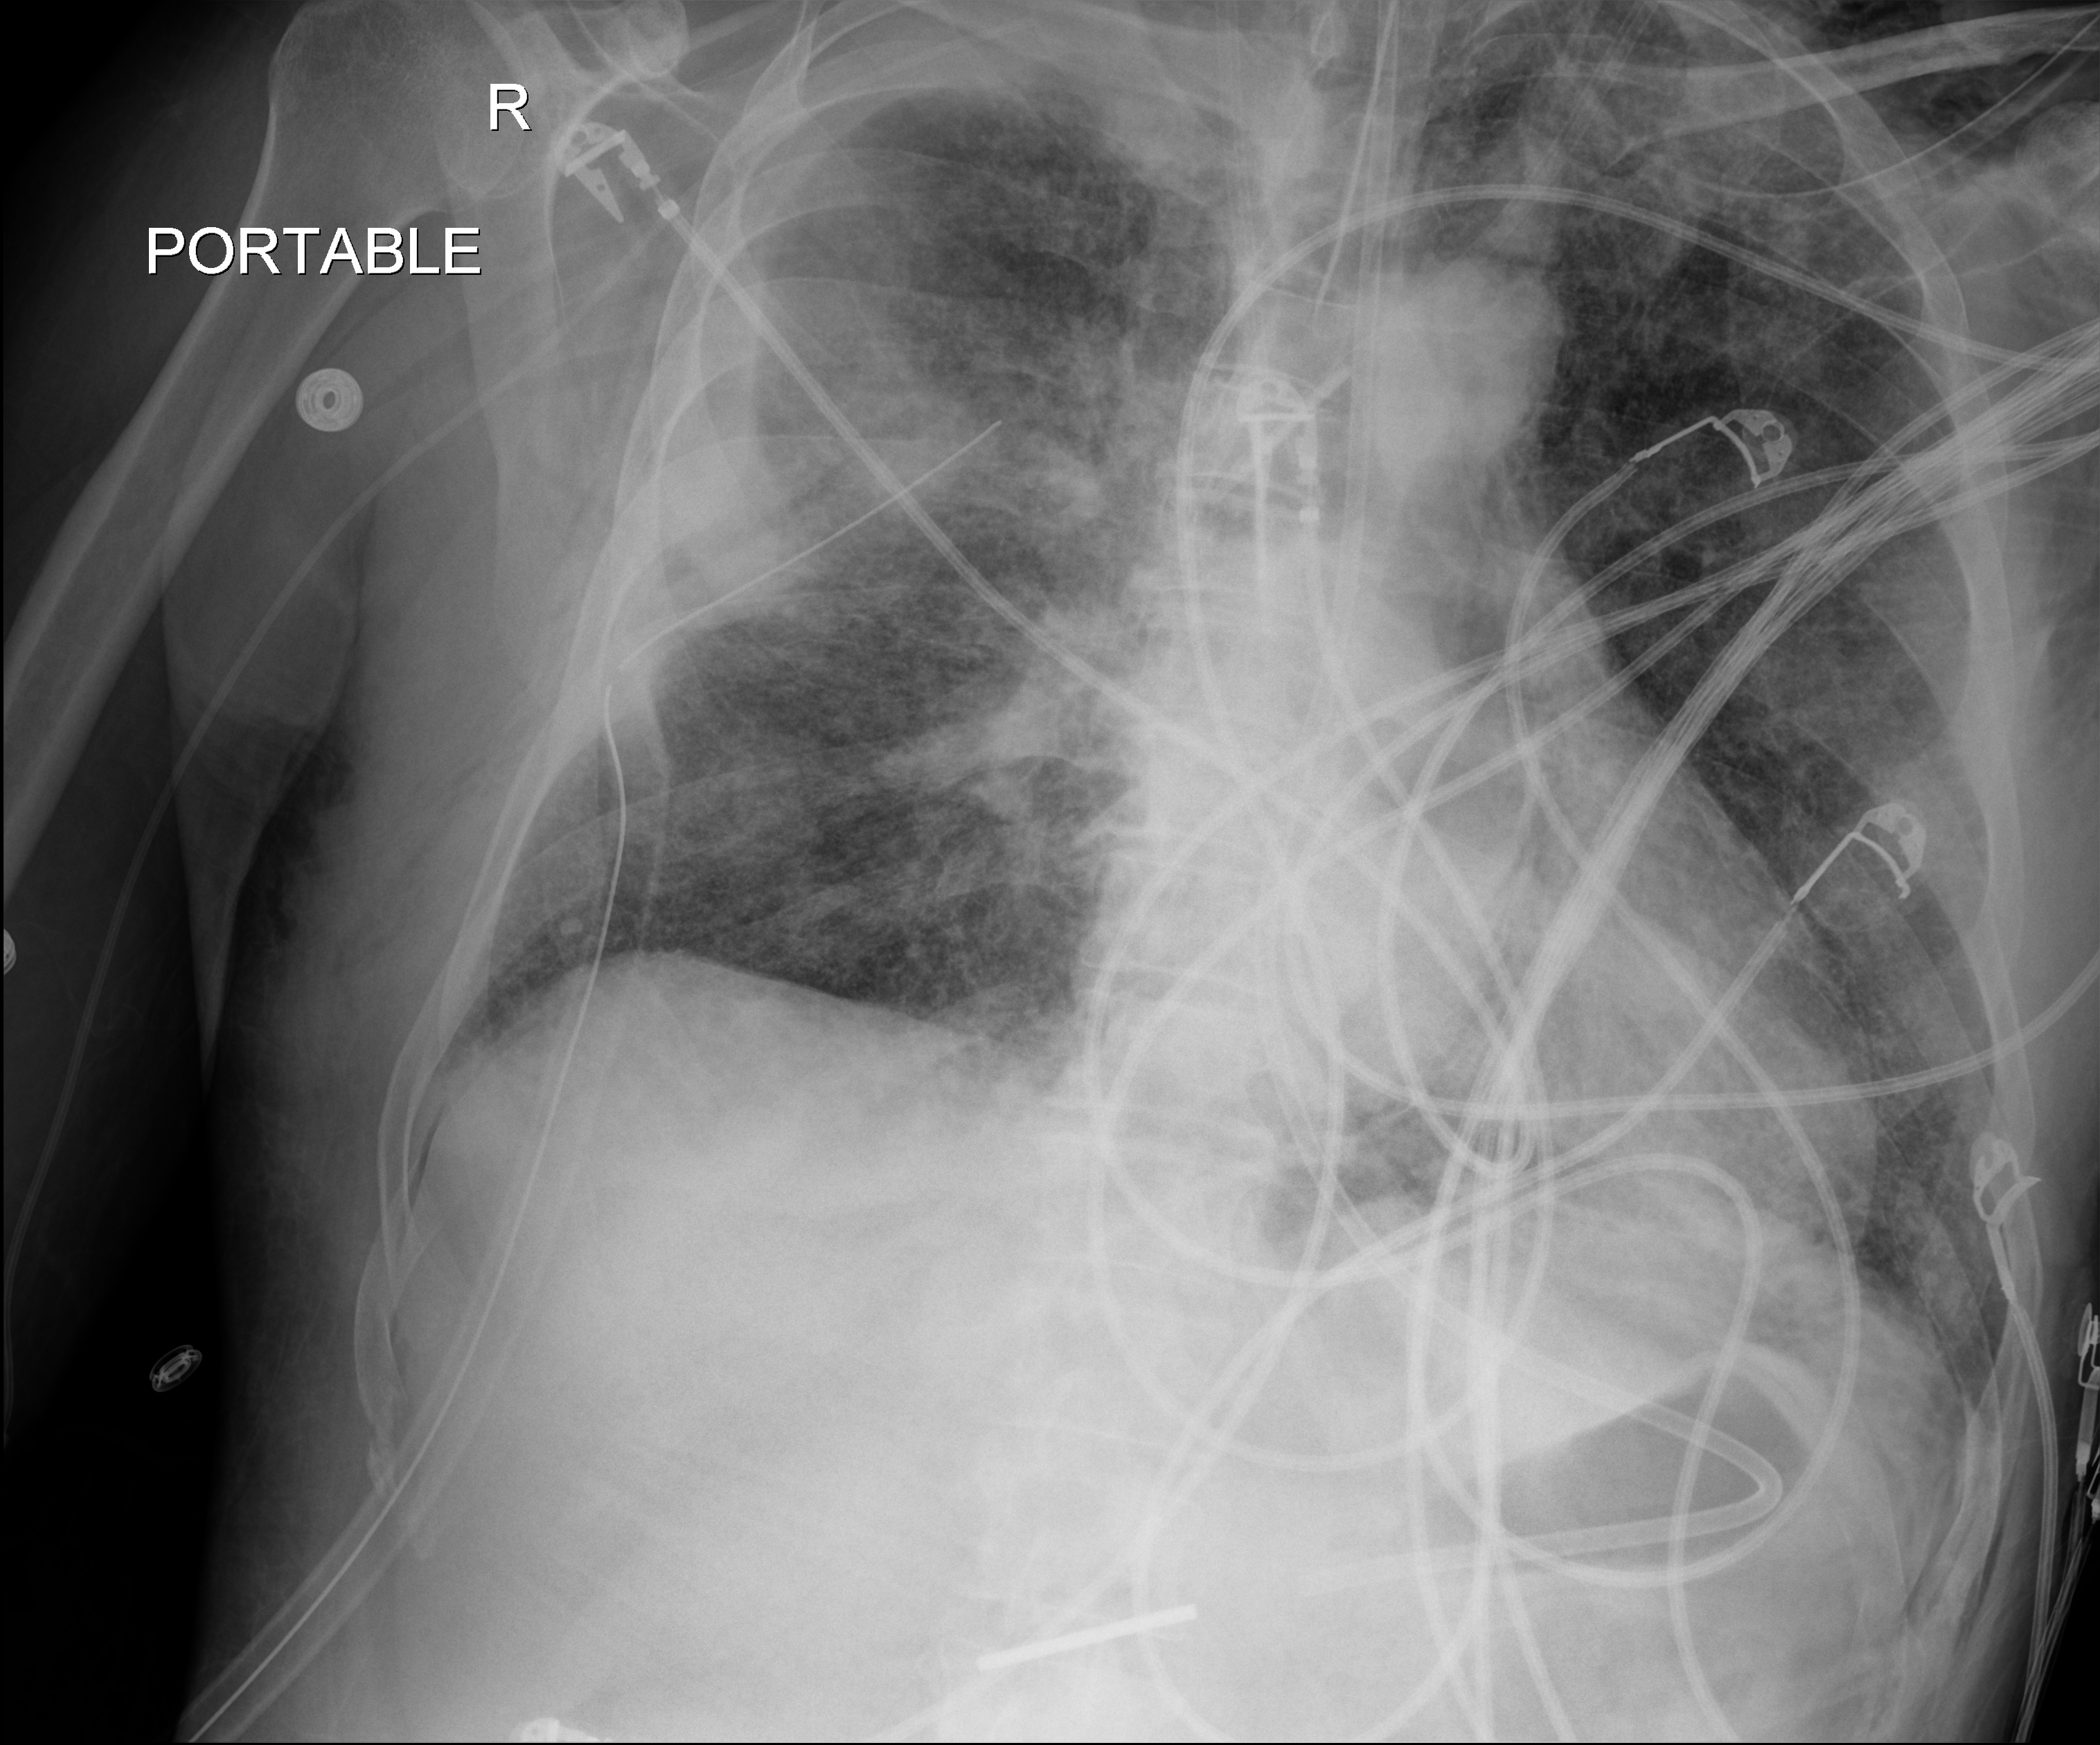
Portable chest radiograph. Patient hospitalised with COVID-19; male, aged 18–59 years.
Admission-level facts for this patient (not findings on this image; timing relative to this image not recorded): length of hospital stay: 42 days; mechanically ventilated during this hospital stay: yes; admitted to intensive care during this hospital stay: yes.